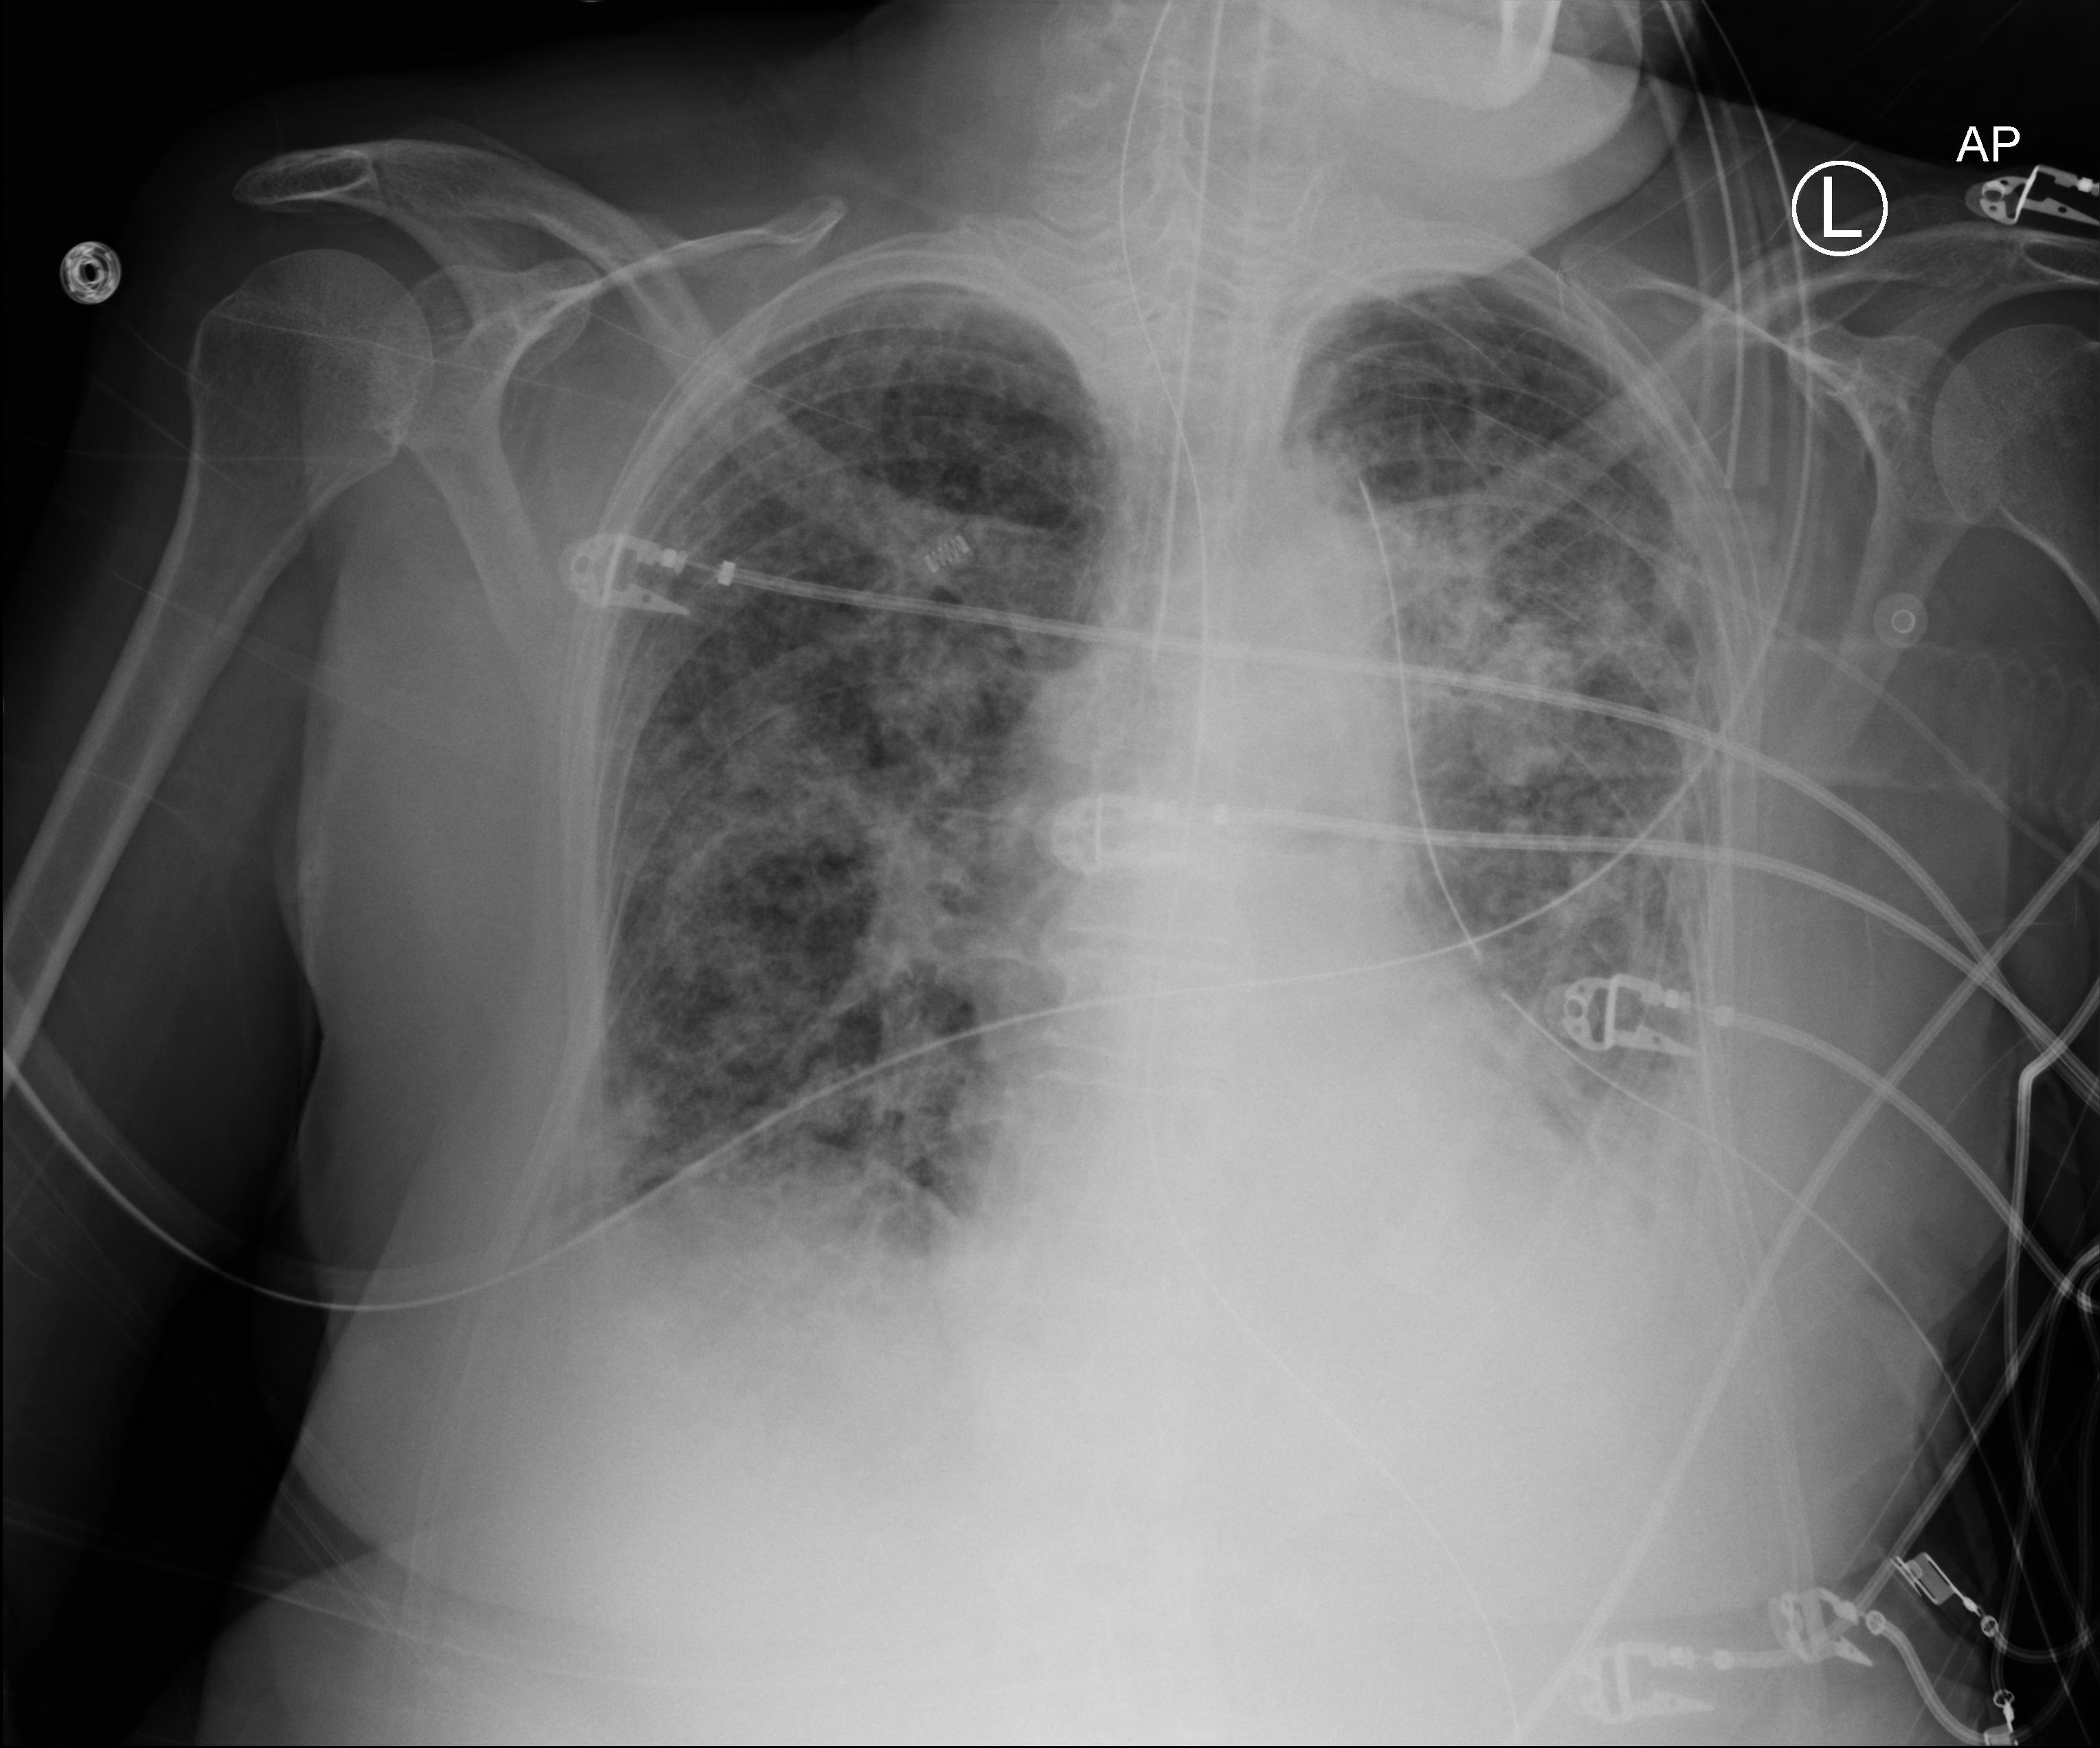
Portable chest radiograph; anteroposterior (AP) projection. Patient hospitalised with COVID-19; female, aged 75–90 years.
From the hospital-stay record, not from the radiograph (when in the stay this image was taken is not recorded): other chronic lung disease (admission record): yes; length of hospital stay: 70 days.